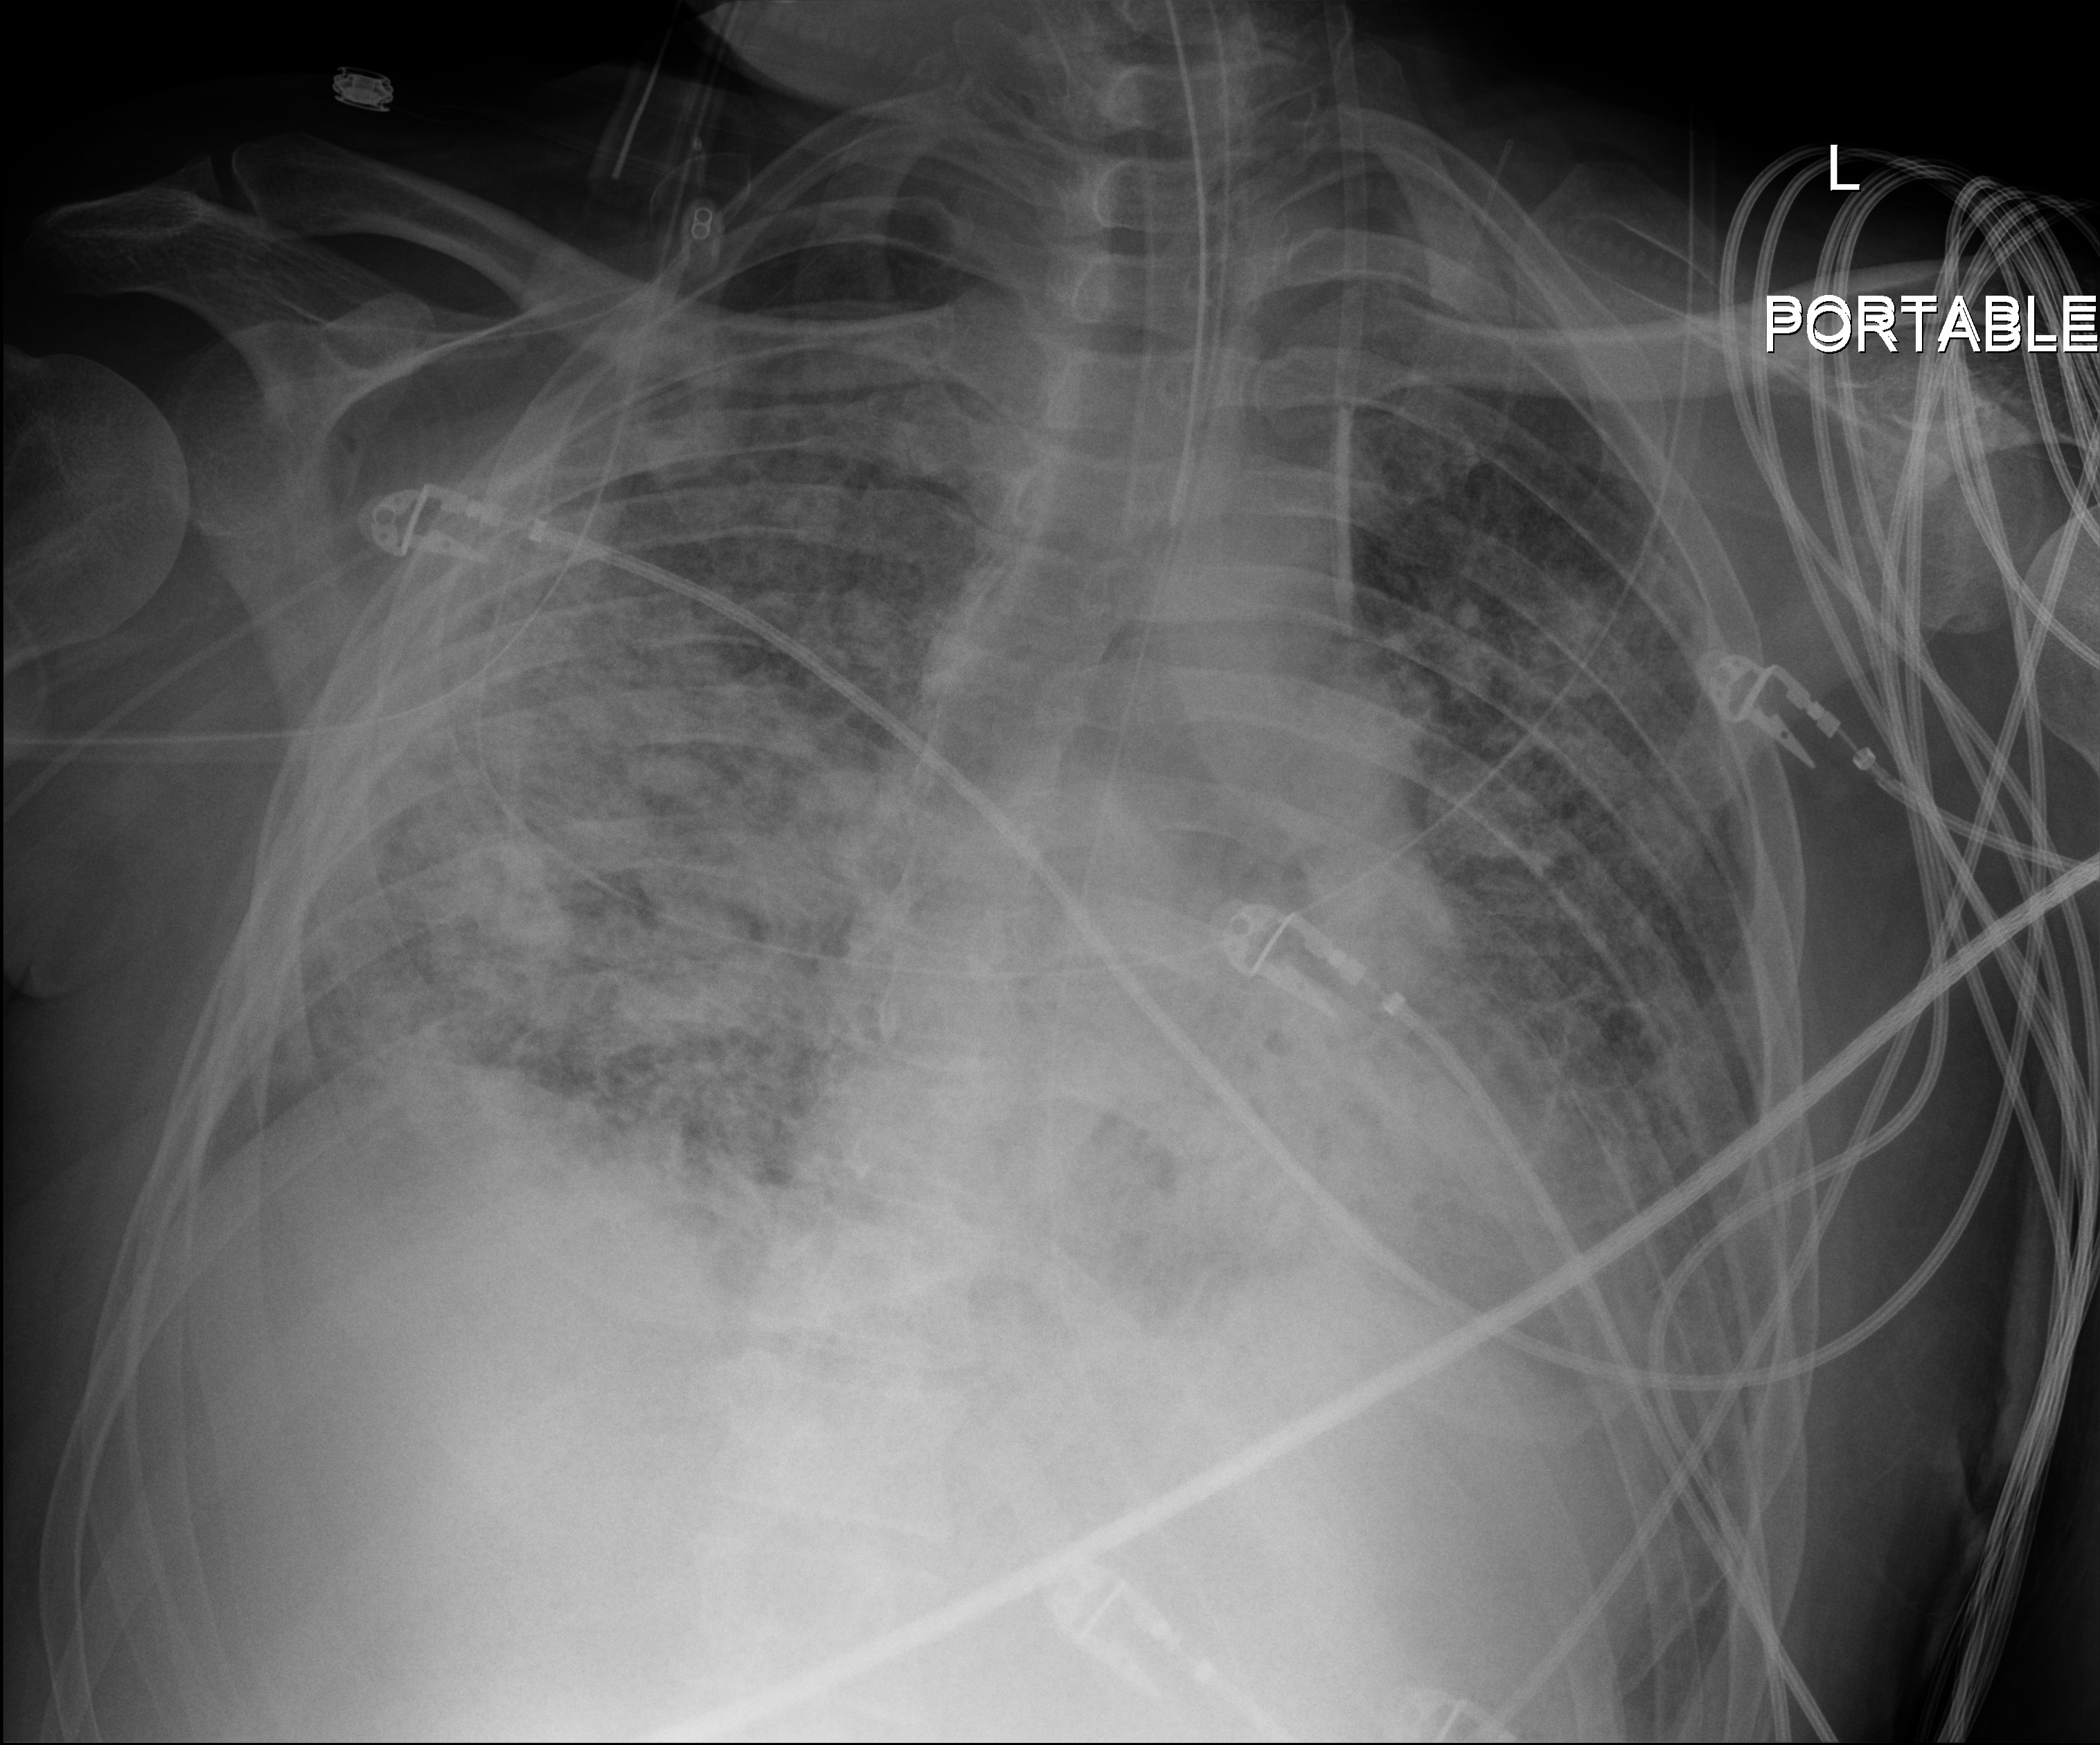
Chest X-ray (portable), anteroposterior (AP) projection. Male patient hospitalised with COVID-19, age 18–59 years.
From the hospital-stay record, not from the radiograph (when in the stay this image was taken is not recorded): admitted to intensive care during this hospital stay: yes; mechanically ventilated during this hospital stay: yes.